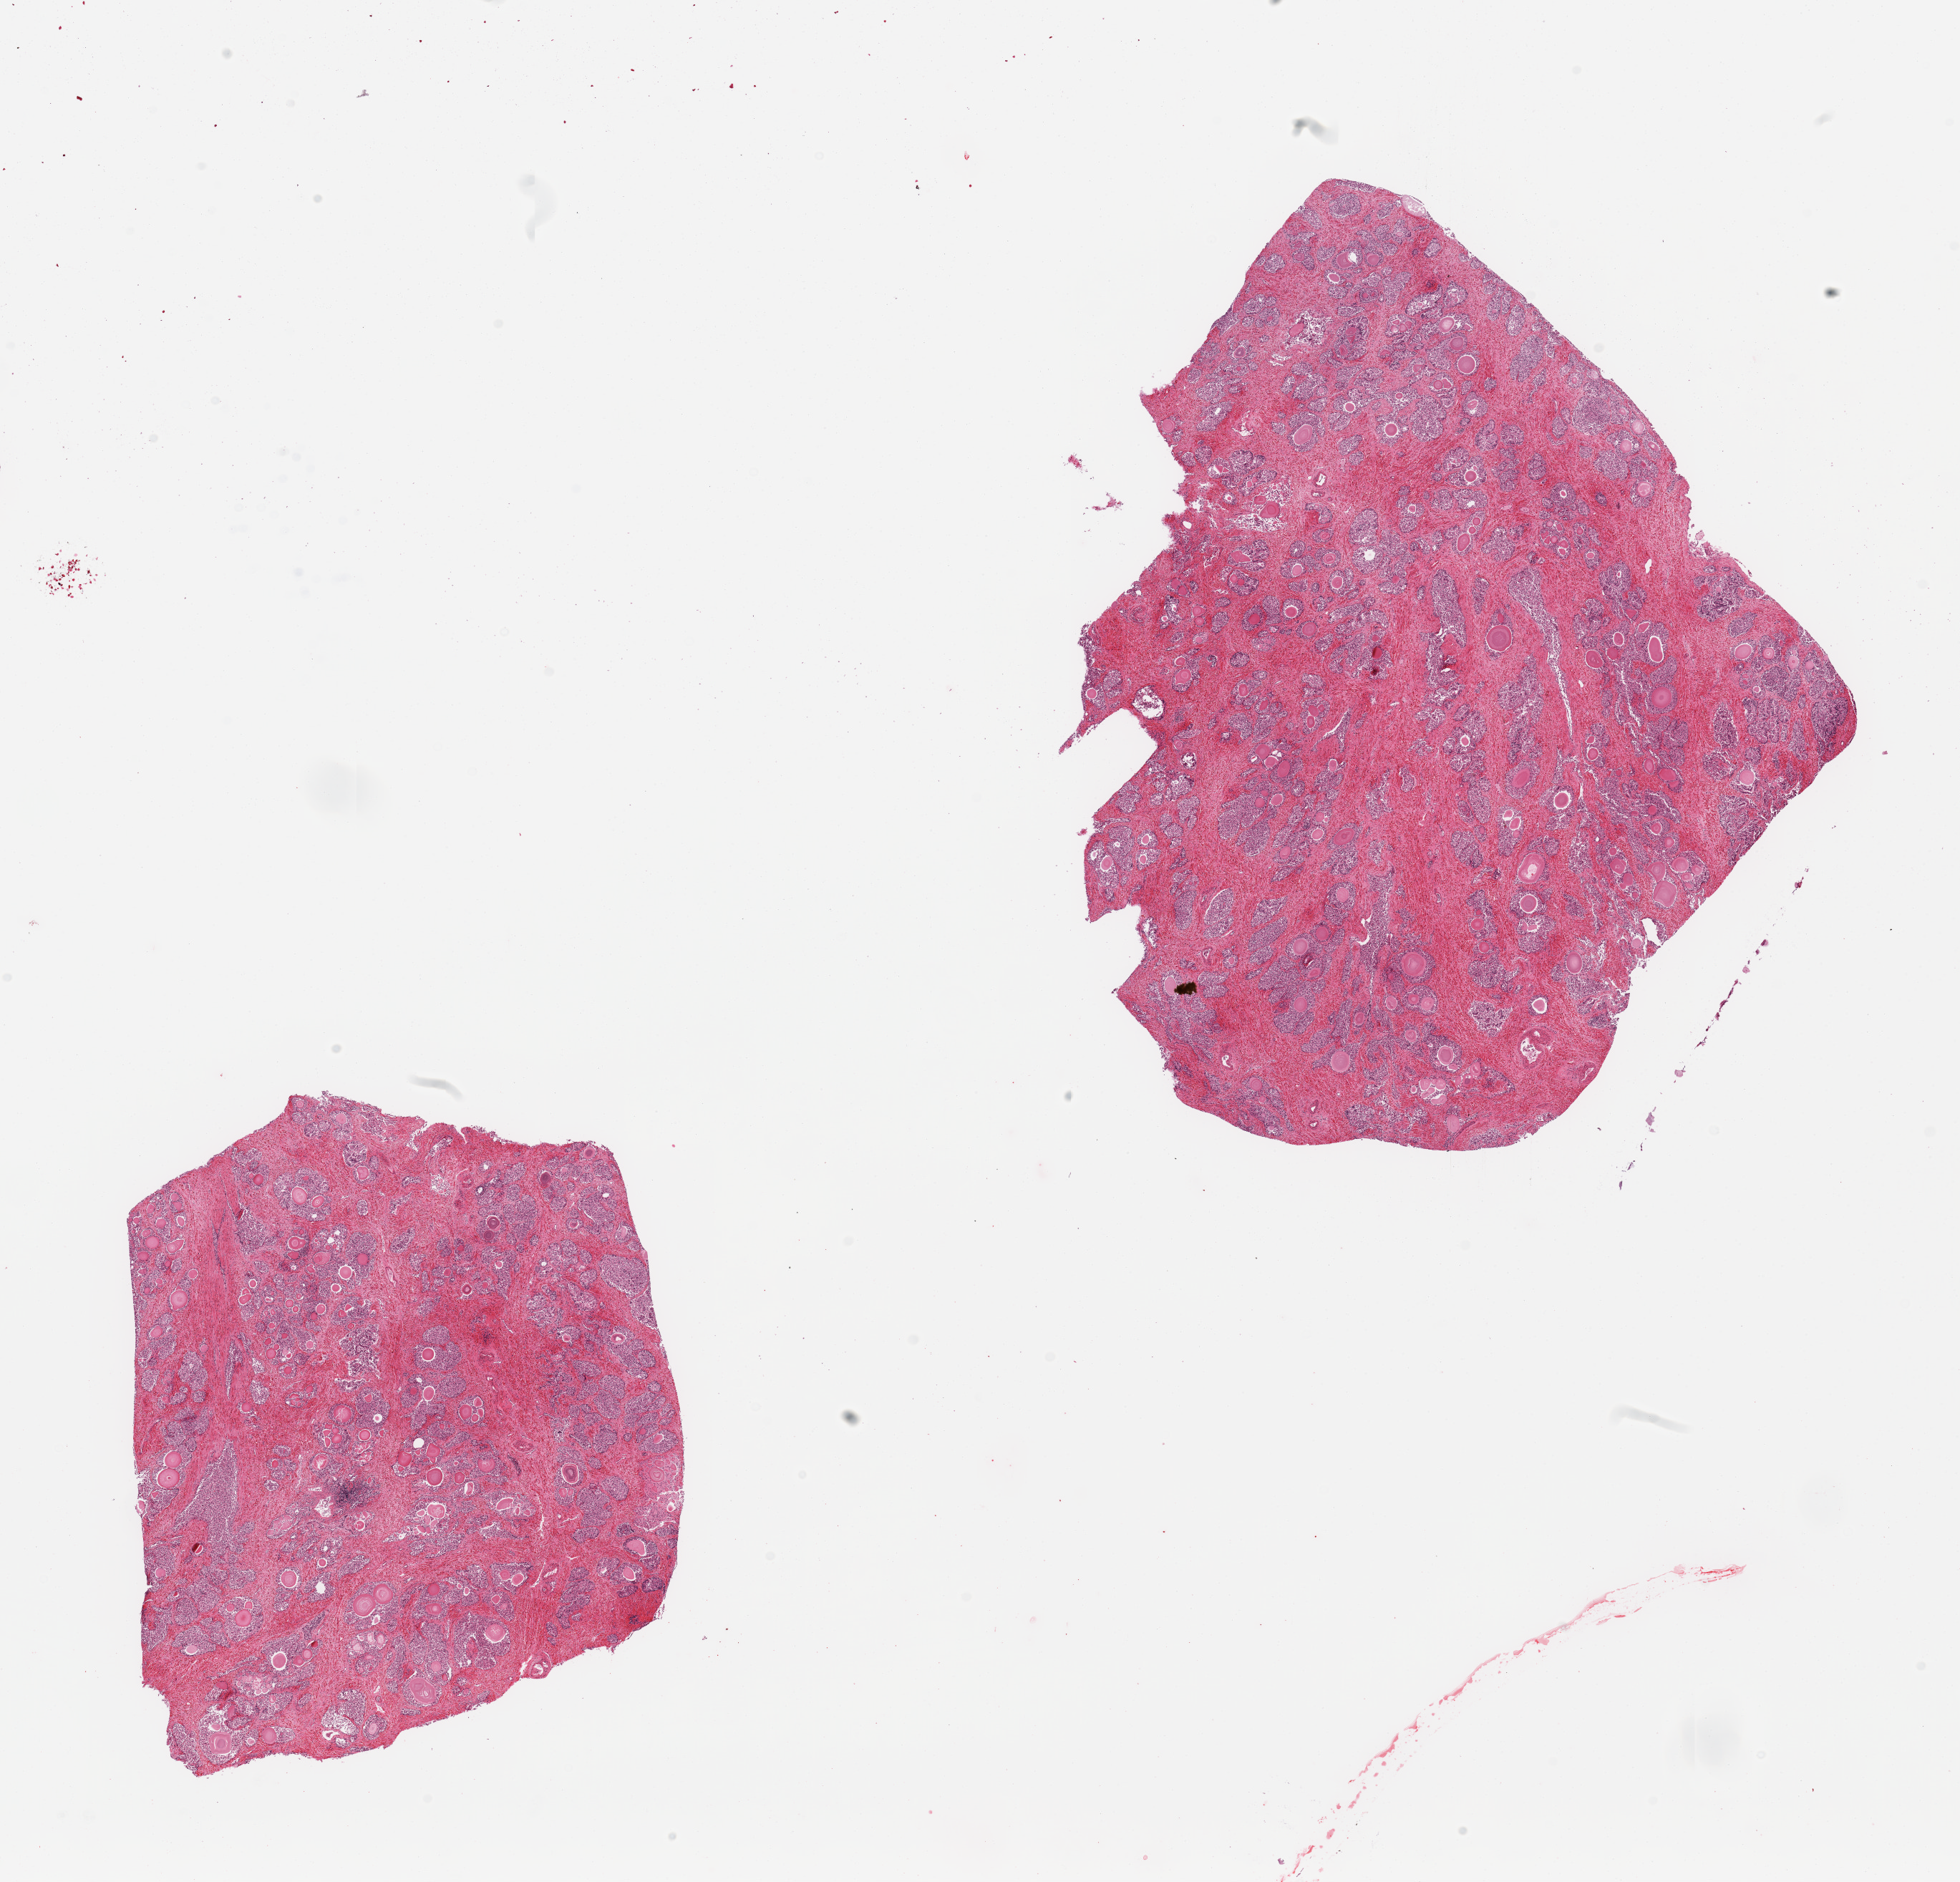
Haematoxylin and eosin whole-slide image — shown as a low-resolution overview of the whole scanned area (about 21.7 x 20.8 mm). PAXgene-fixed paraffin-embedded (PFPE) section. Target tissue: prostate. Tissue donor sample. Donor: male.
Review note (as recorded): 2 pieces; fibromuscular stroma with glands with sloughed lining, numerous corpora amylacea.